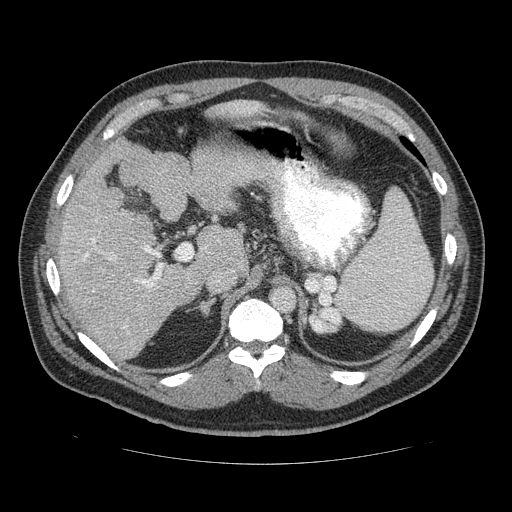
Contrast-enhanced abdominal CT (liver protocol), one axial slice. Position 85 of 113 along the scan axis. Reconstruction kernel STANDARD. Soft-tissue window (W 400 / L 40 HU). 2.5 mm slice thickness. 512 × 512 image matrix. Case-level facts recorded for this patient, not image findings: diagnosis: hepatocellular carcinoma (patient treated with transarterial chemoembolisation; whether this scan precedes or follows treatment is not stated here); TNM stage (as recorded): Stage-II; Child-Pugh class: B; tumour differentiation: moderately differentiated.
Annotated regions visible in this slice (semi-automatic segmentation, software-assisted and operator-edited):
- liver parenchyma outside the tumour (the mass and vessels are separate outlines, so this box may not span the whole liver): box from (x=50, y=100) to (x=356, y=360) px
- liver vessels: (x=83, y=211)–(x=215, y=330)